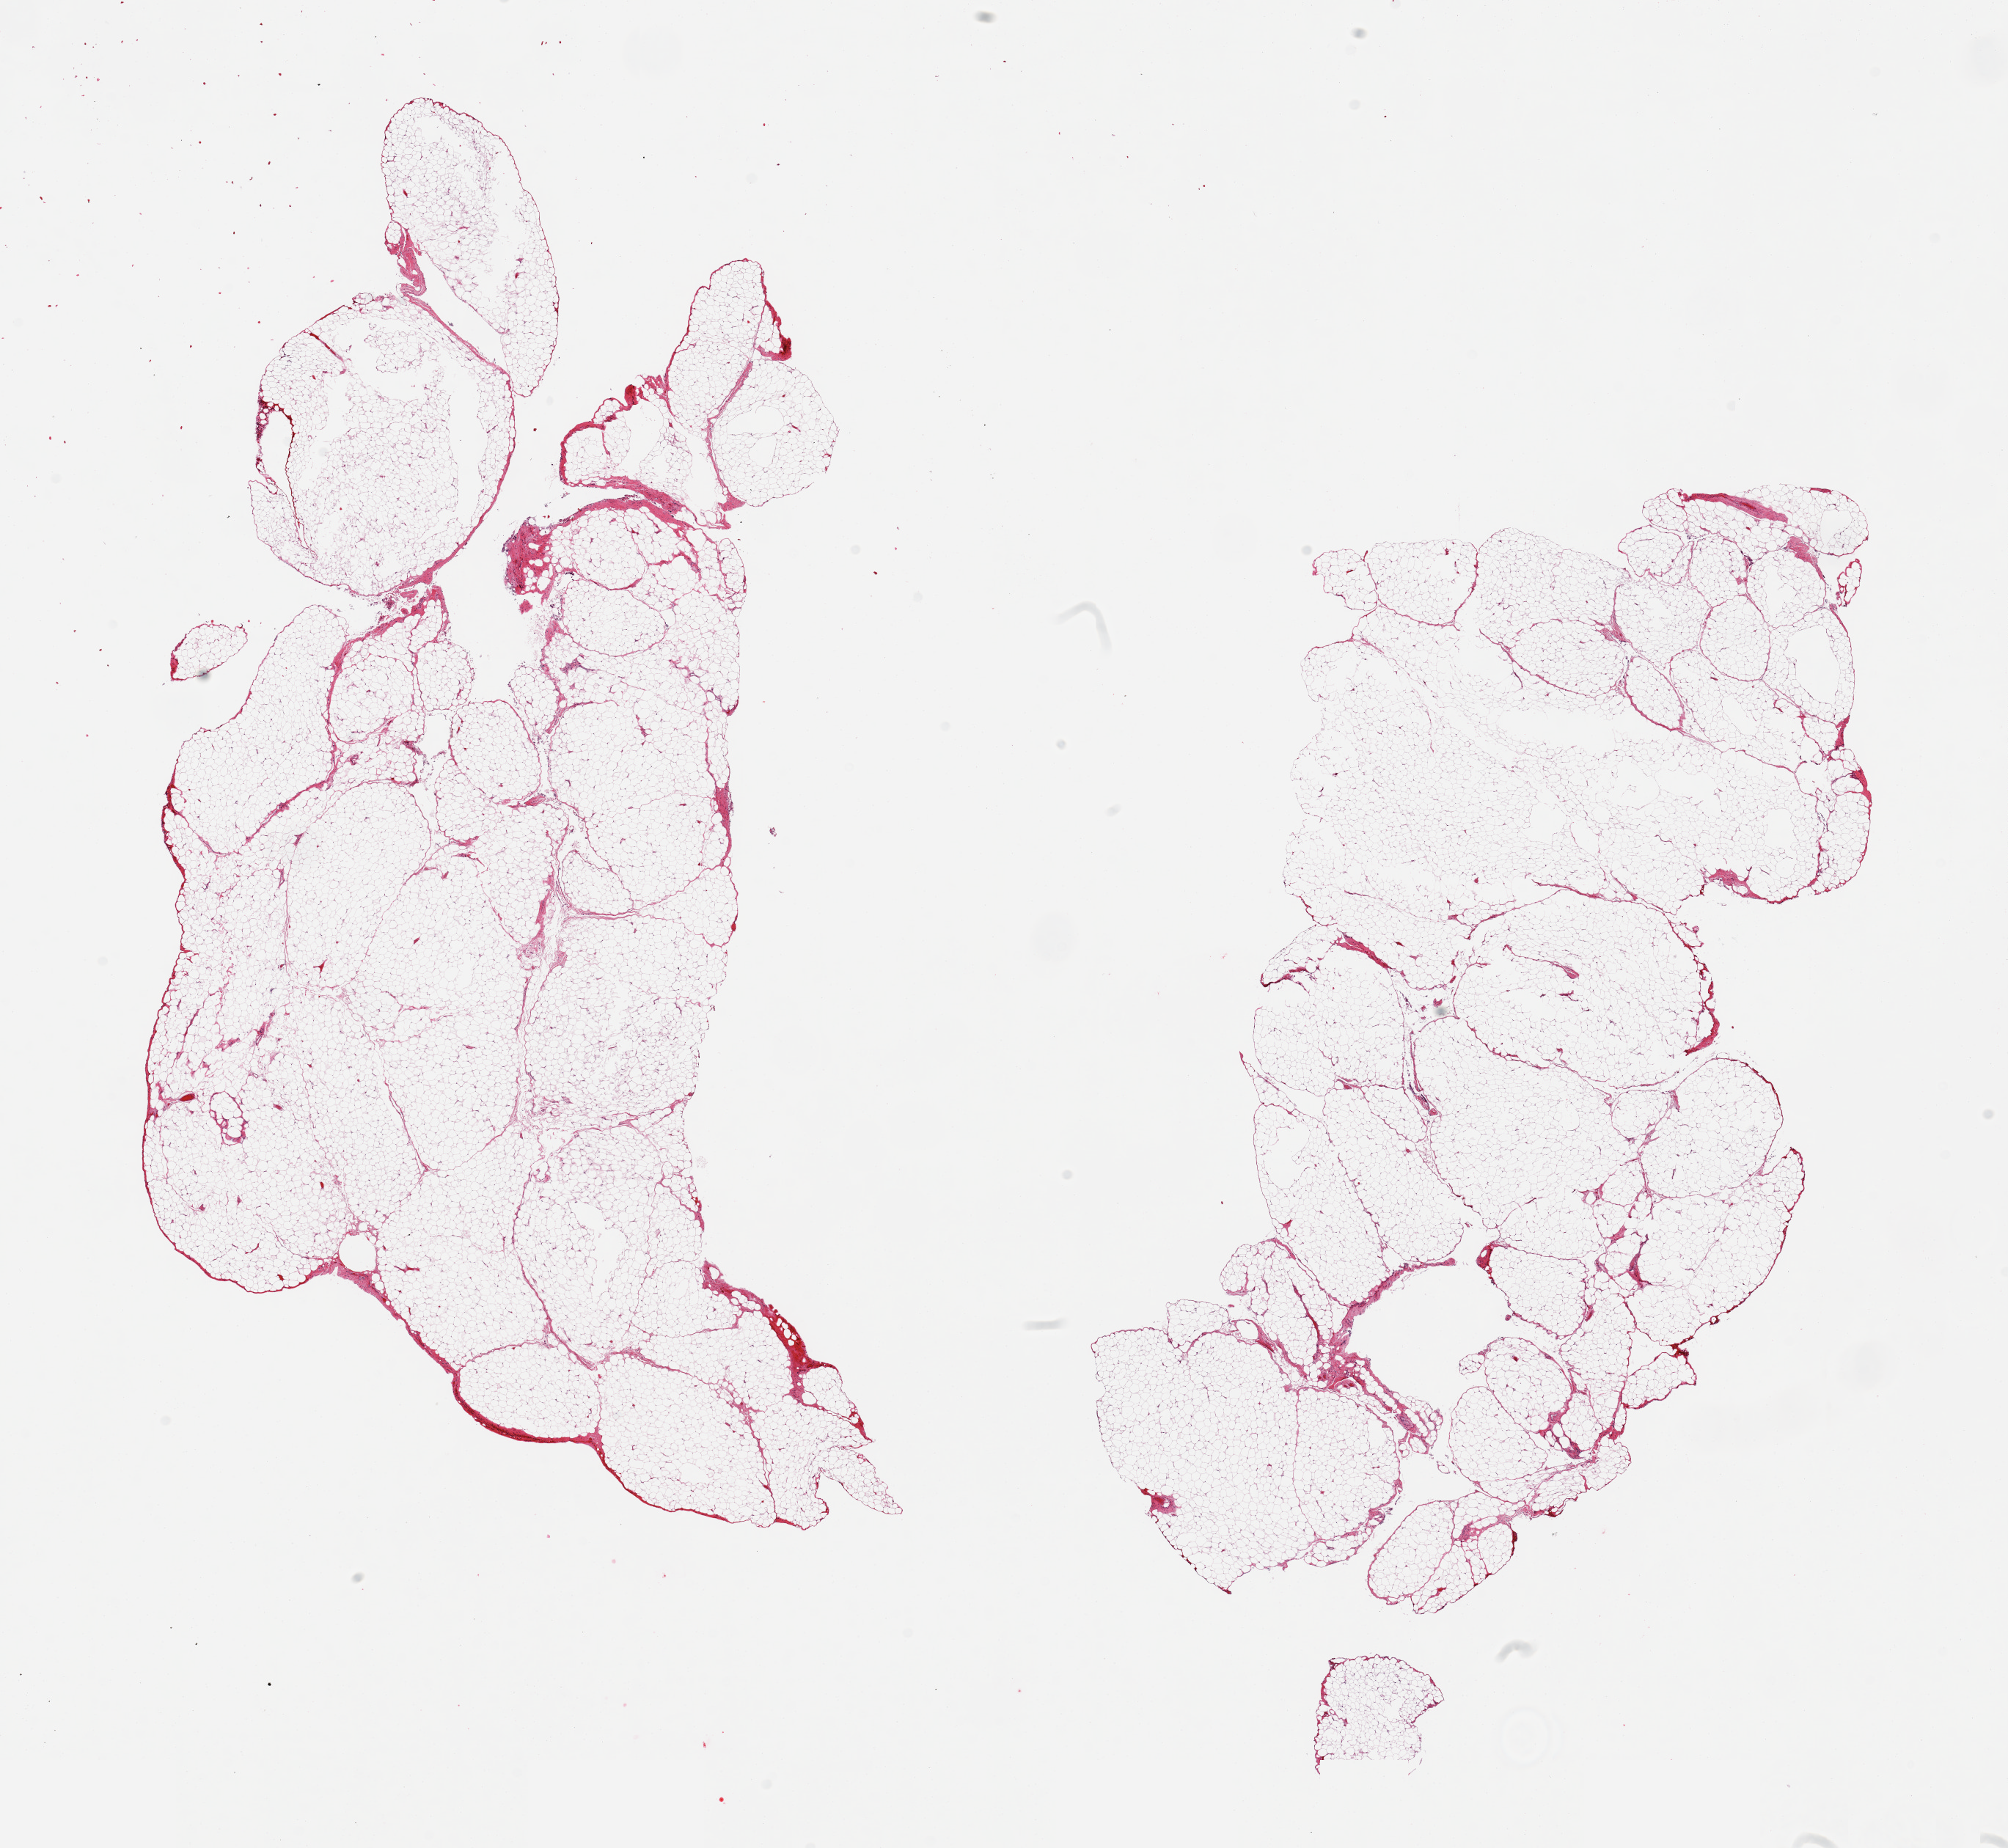
Whole-slide image, haematoxylin and eosin stain — low-resolution overview of the scanned area, about 21.7 x 19.9 mm; PAXgene-fixed, paraffin-embedded tissue; sampled site (target tissue): omentum; tissue donor sample.
• pathologist's review note for this sample: 2 pieces